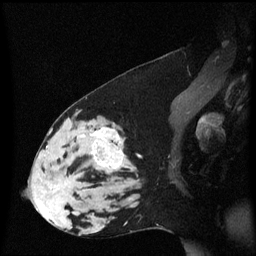
Breast MRI (dynamic contrast-enhanced), one sagittal slice. Slice 33 of 60 in the series (ordered by position). Dynamic contrast-enhanced series, image 2 of 3 at this slice position (ordered by acquisition). 1.5 T. TE 4.2 ms, TR 8.4 ms. 256 × 256 image matrix, field of view 210 × 210 mm. Patient: female, 33 years. From the clinical record (not read from this slice): setting: breast cancer imaged before/during neoadjuvant chemotherapy; receptor status: triple-negative.
Structures marked on this image (semi-automatic segmentation, software-assisted and operator-edited):
- analysis volume of interest (the breast-tissue region the enhancement analysis was run in; not a lesion): box from (x=44, y=123) to (x=139, y=189) px
- tumour enhancement mask (voxels above the 70 % enhancement threshold inside the analysis volume of interest): (x=81, y=128)–(x=125, y=173)